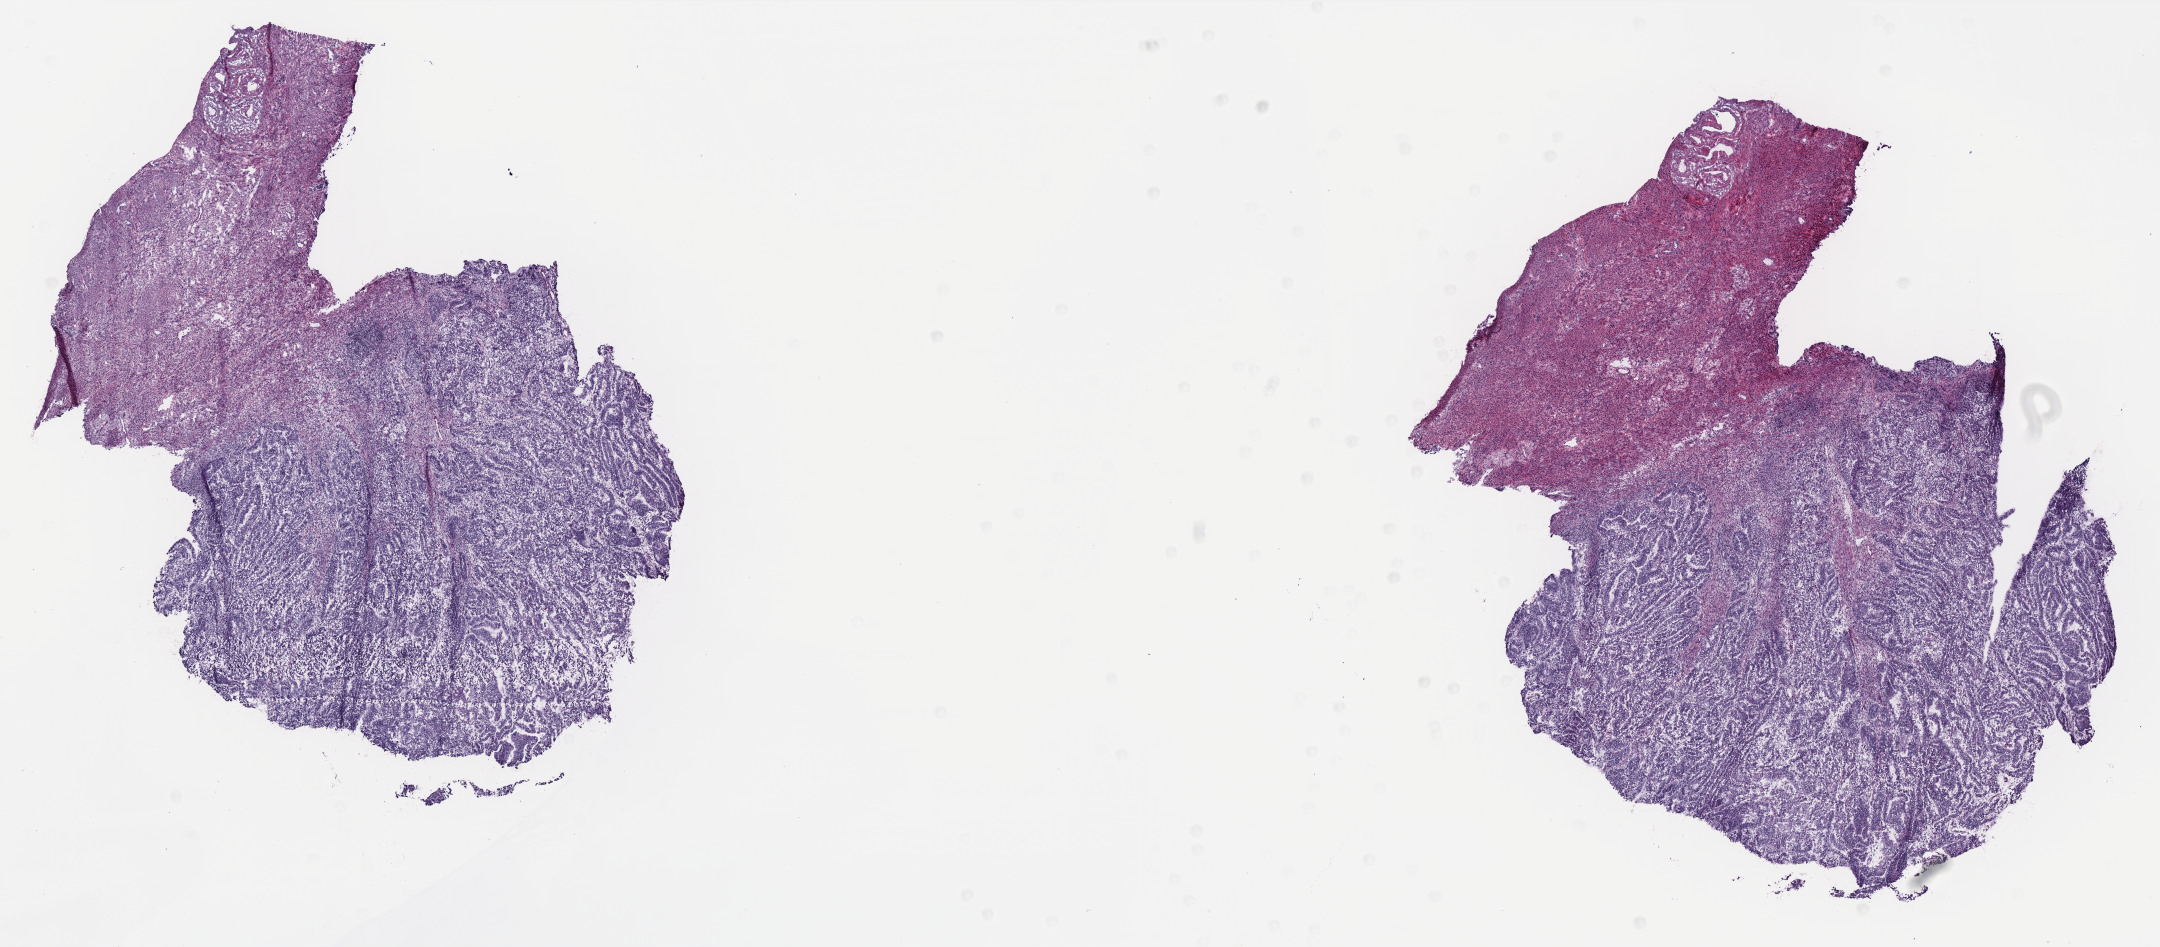
Whole-slide histology image, H&E — a low-resolution overview of the entire scanned area, about 17.3 x 7.6 mm, frozen section from the bottom of the tissue portion, sample: primary tumour, uterus. Female, age 76 years at initial diagnosis. Histologic grade: G1 (well differentiated). Composition of this section per pathologist review: tumour cells 60%, tumour nuclei 50%, normal cells 30%, stromal cells 10%, necrosis 0%. Inflammatory infiltration, as recorded: lymphocyte infiltration 0%, monocyte infiltration 0%, neutrophil infiltration 0%.
Pathologic diagnosis: Endometrioid adenocarcinoma, NOS (endometrium). FIGO stage: IA. Lymph nodes positive (case pathology): 0 of 13 examined.